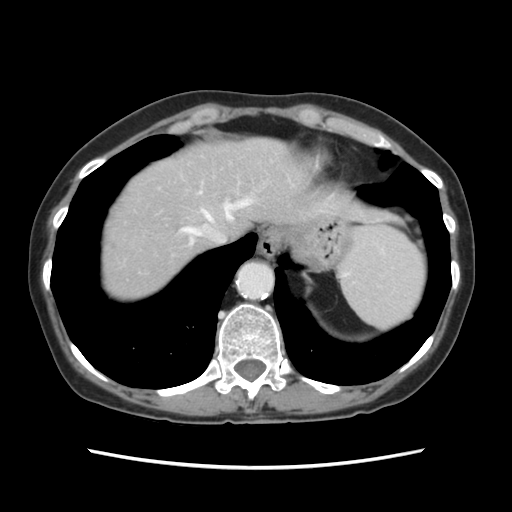
Contrast-enhanced abdominal CT, one axial slice. Slice 102 of 120 in the series (ordered by position). 120 kVp. Intravenous contrast given. Soft-tissue window (W 400 / L 40 HU). 512 × 512 image matrix. Female patient, age 70 years. From the clinical record (not read from this slice): diagnosis: colorectal cancer liver metastases, imaged before liver resection; multiple liver metastases: no; largest metastasis: 2.5 cm; chemotherapy before resection: yes.
Annotated regions visible in this slice (expert manual segmentation):
- hepatic veins: bounding box [x1, y1, x2, y2] px = [185, 200, 251, 244]
- liver: [101, 139, 310, 297]
- planned liver remnant (the part of the liver to remain after resection): [150, 139, 310, 254]